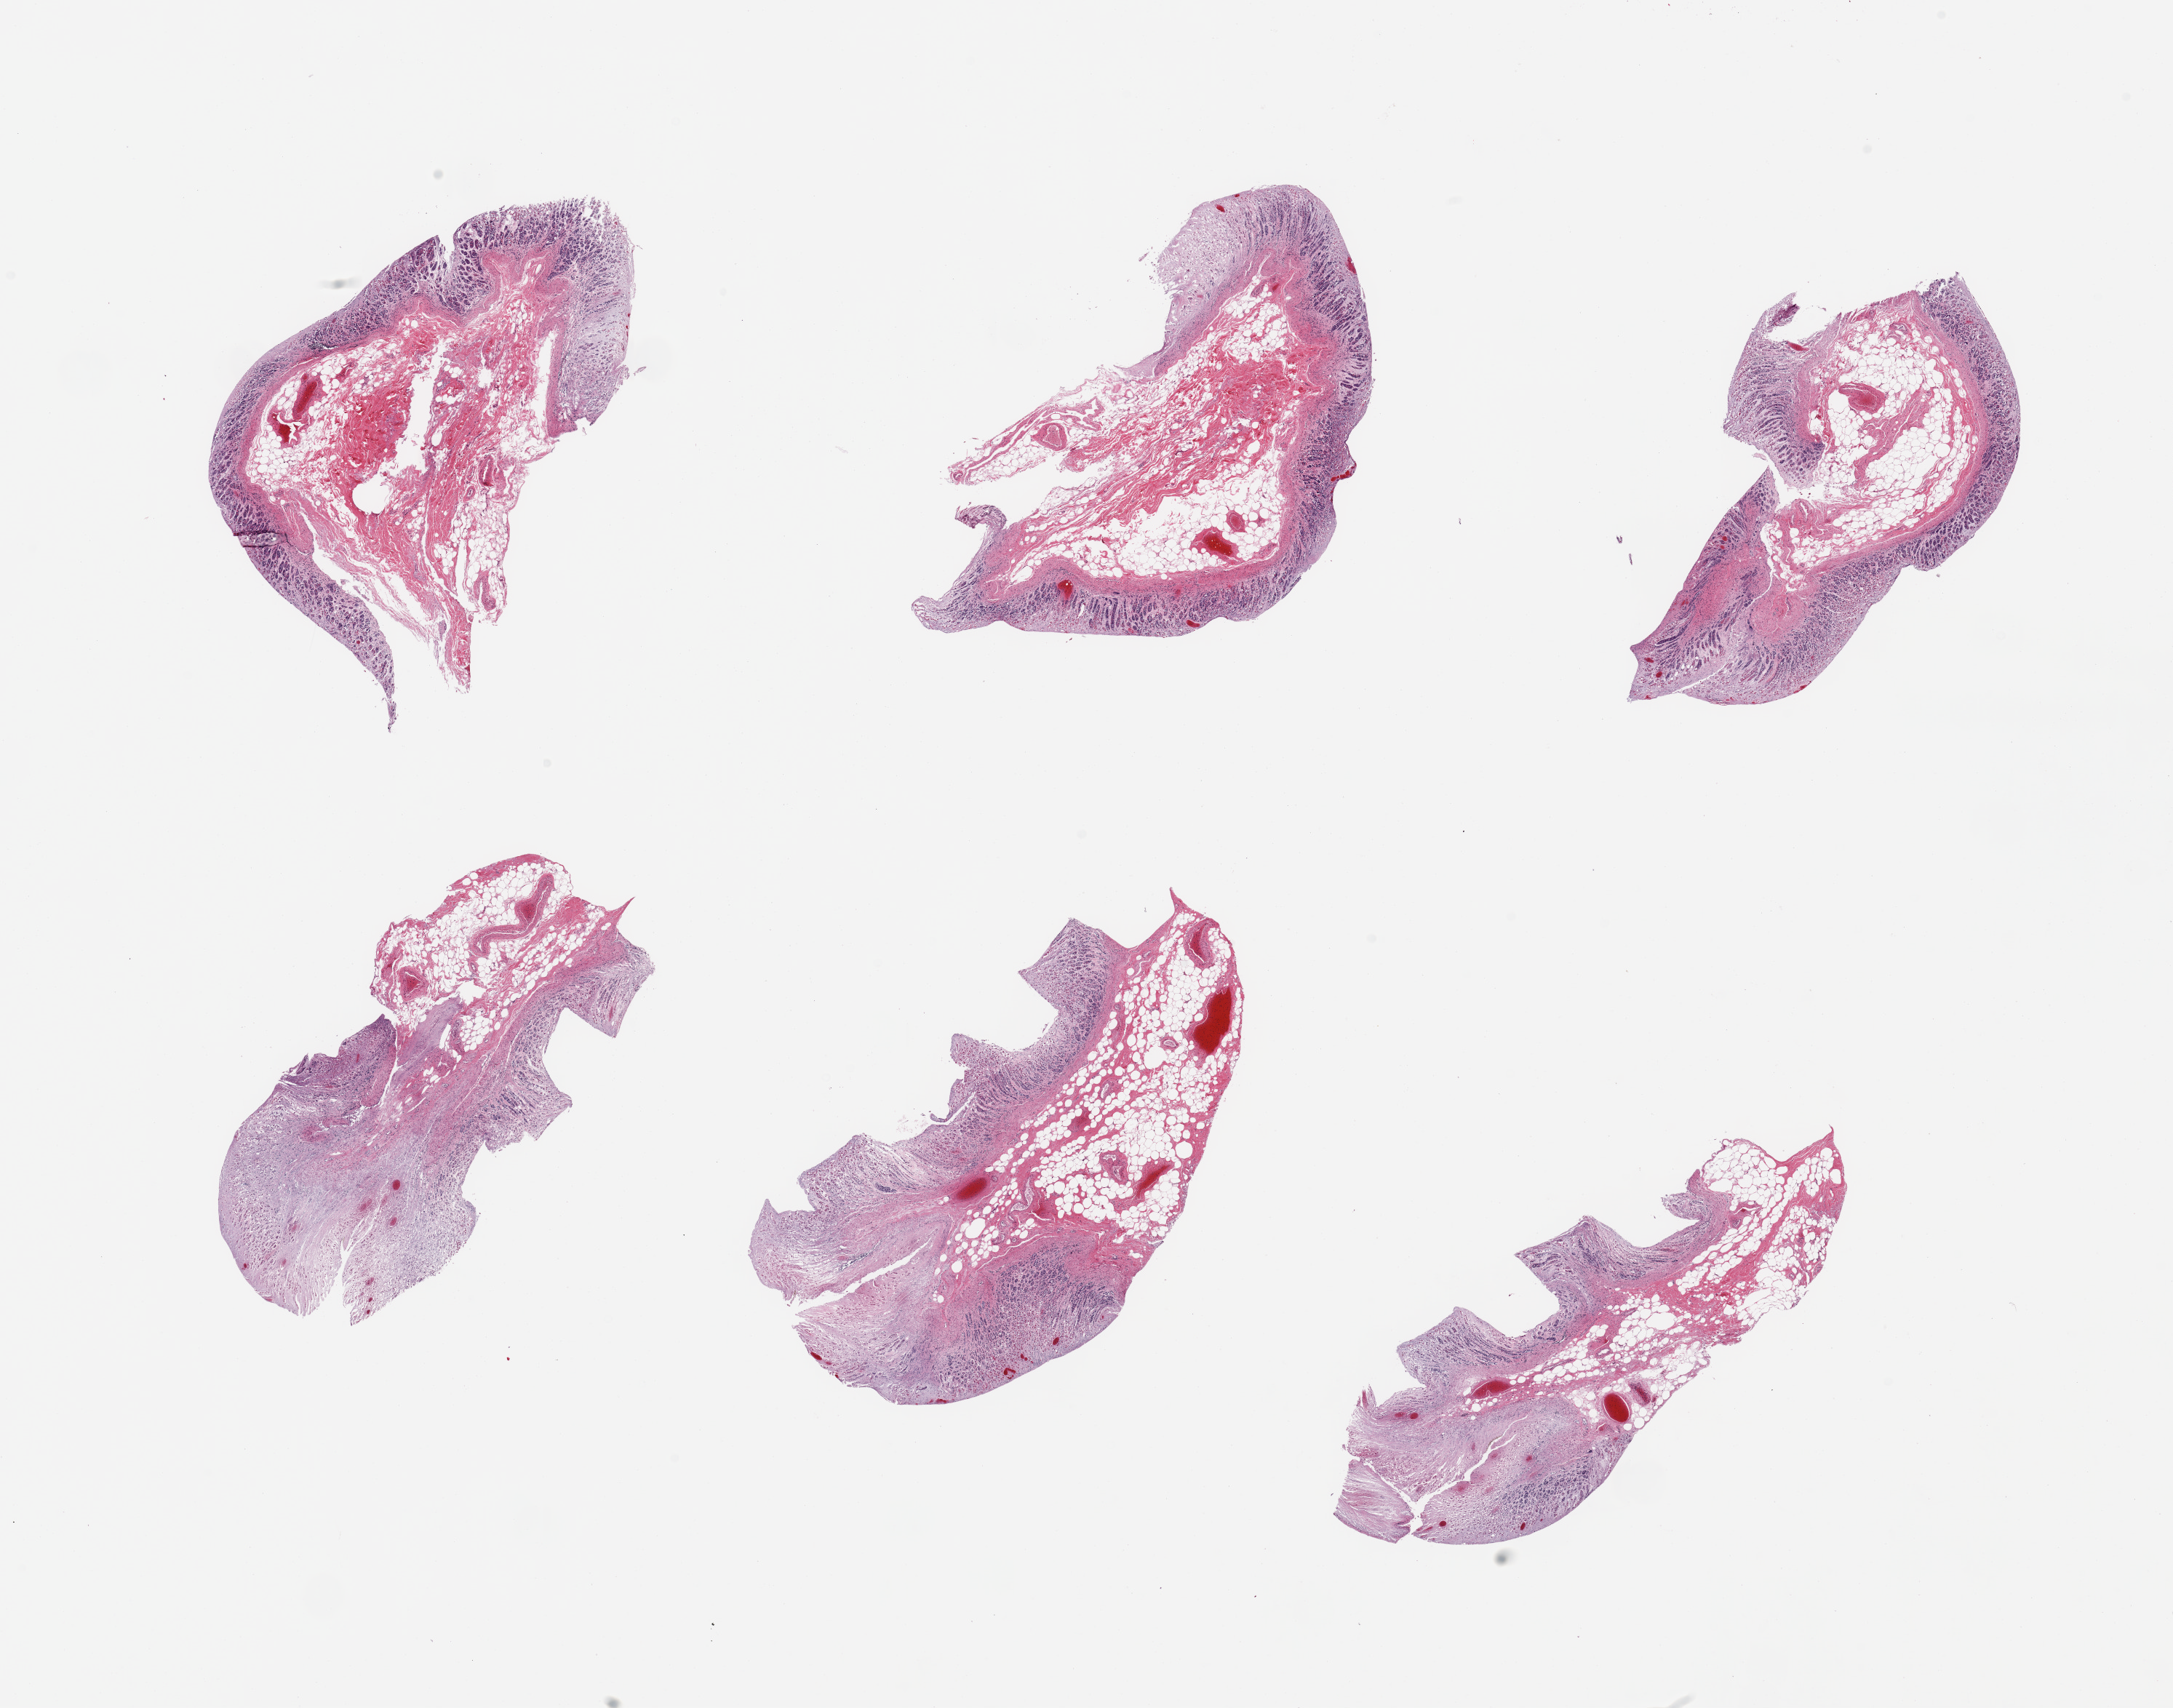
Haematoxylin and eosin whole-slide image, brightfield, whole scanned area (about 23.6 x 18.6 mm) shown as a low-resolution overview. PAXgene-fixed paraffin-embedded (PFPE) section. Sampled site (target tissue): stomach. Tissue donor sample. Male donor.
Pathologist's review note for this sample: 6 pieces; mucosa autolyzed, no muscularis present.